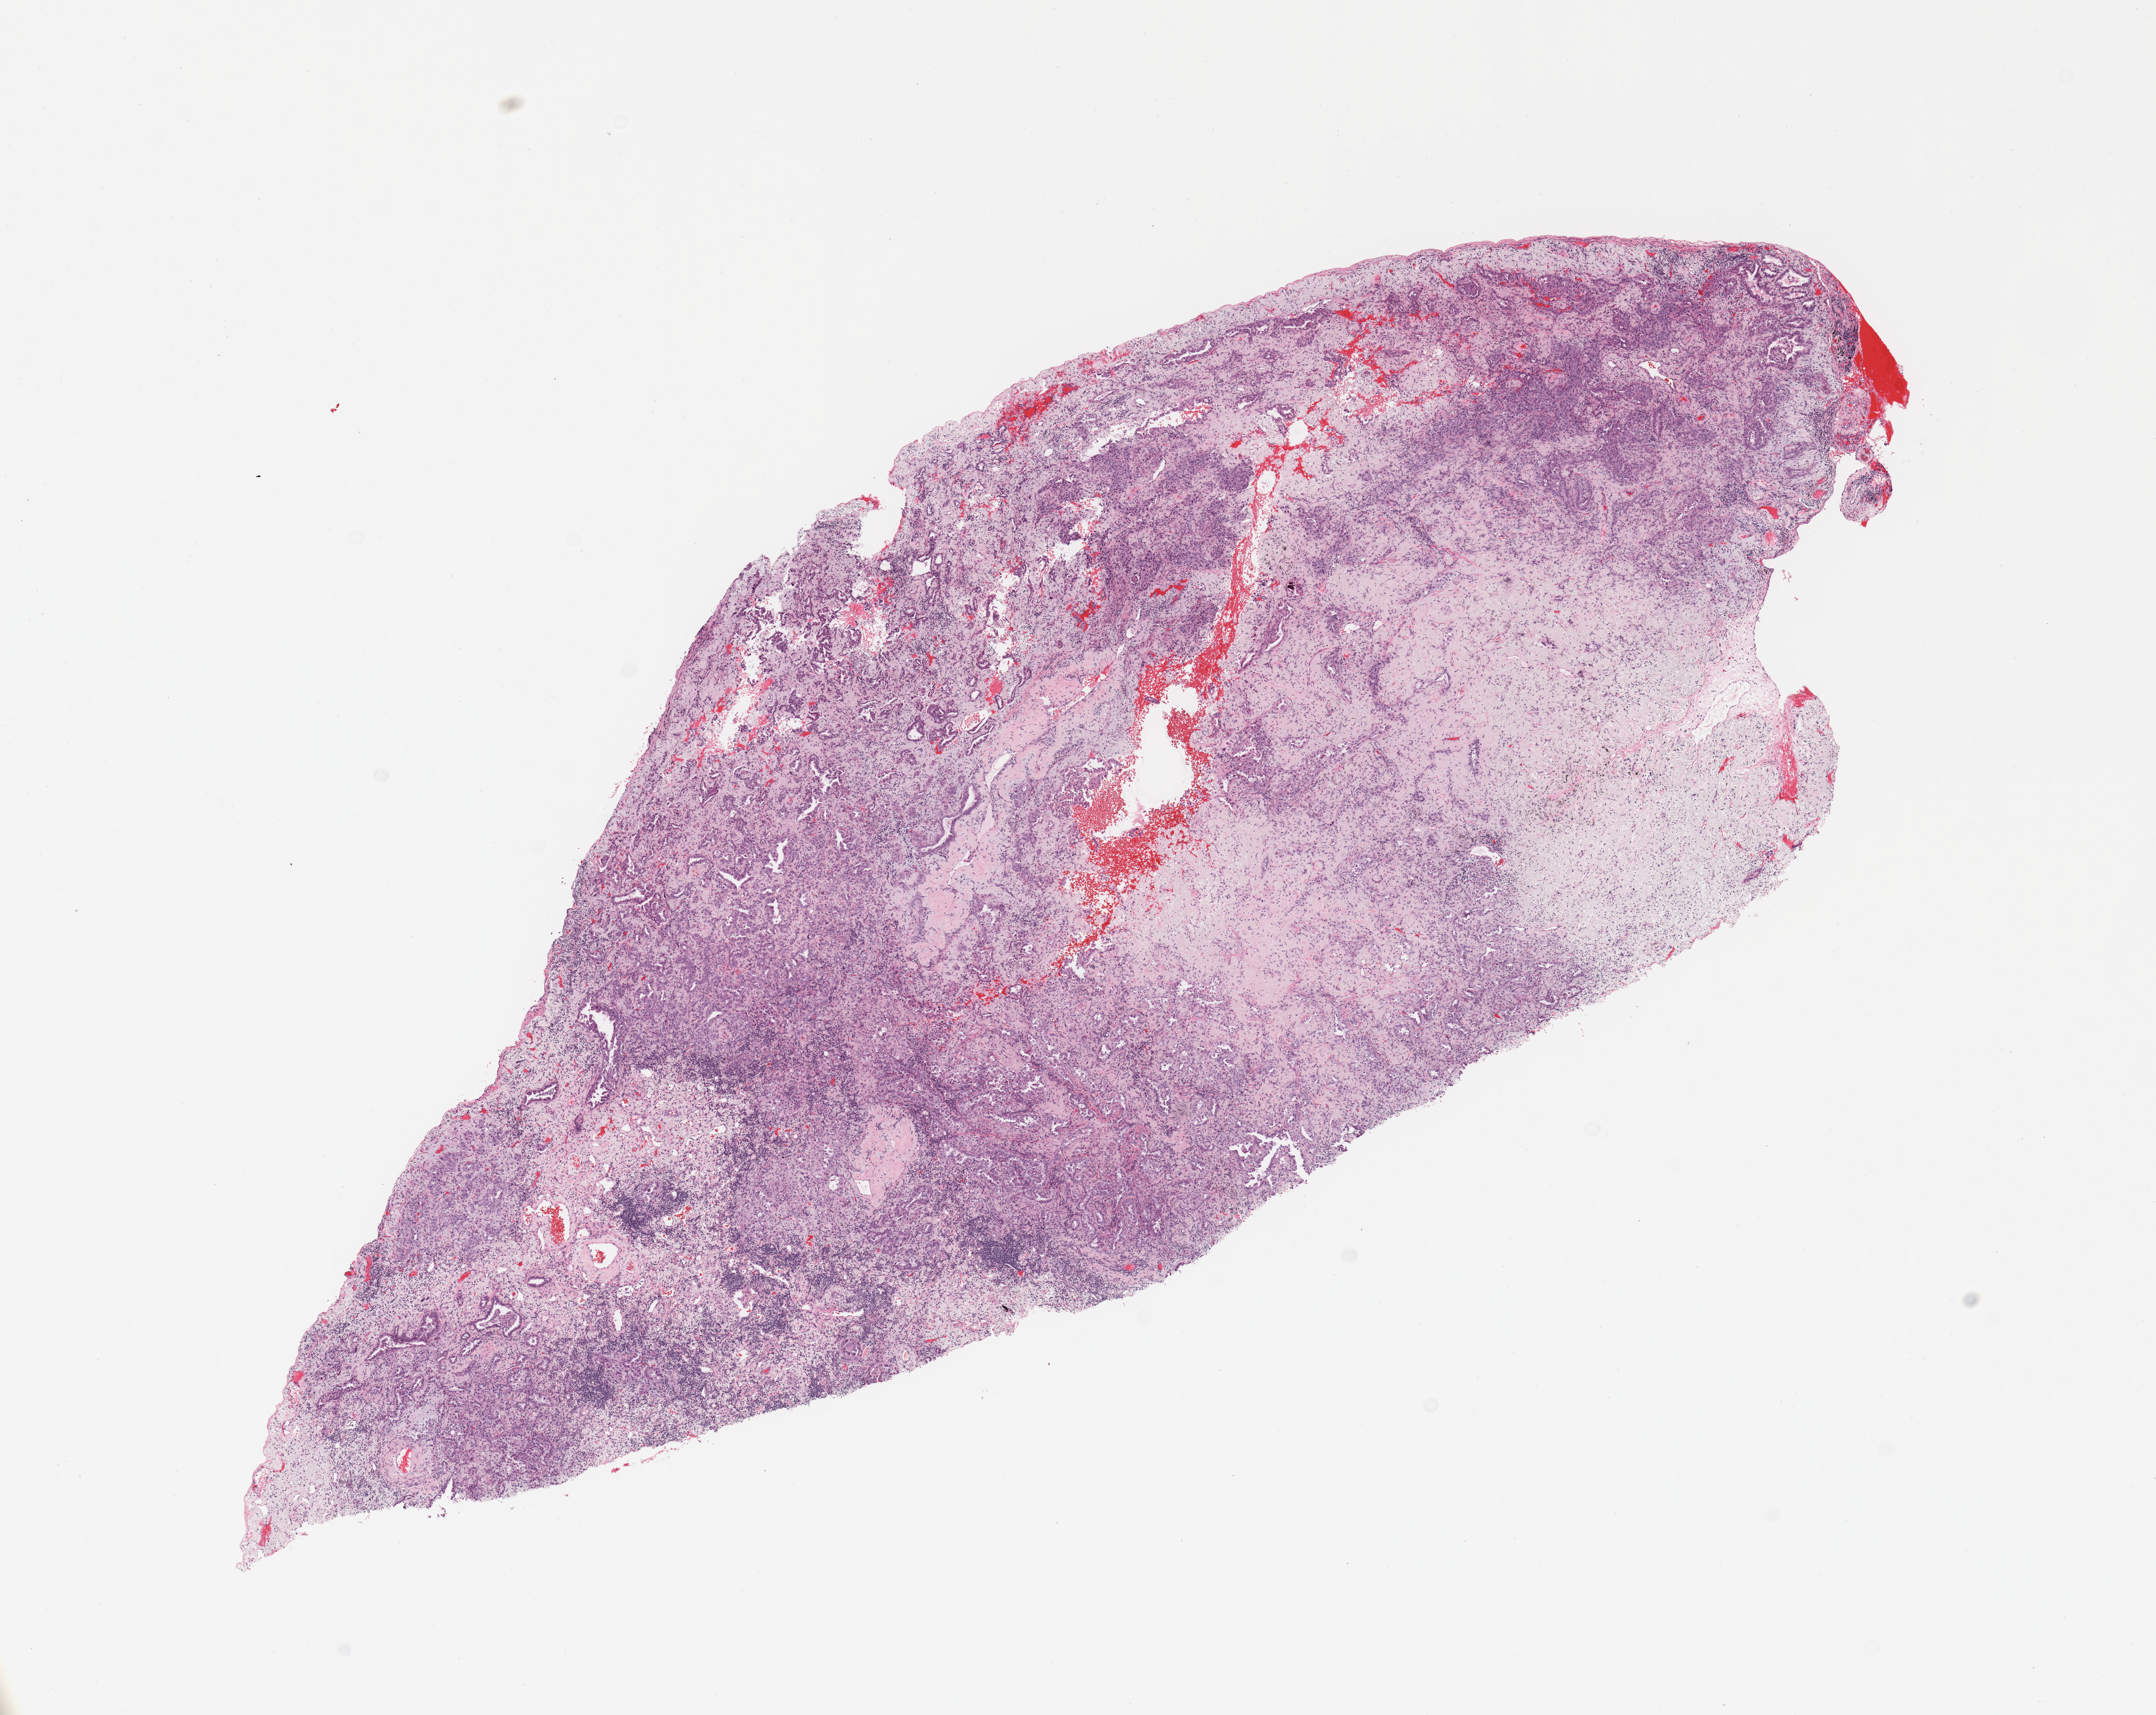
H&E whole-slide image — whole scanned area (about 12.8 x 10.2 mm) shown as a low-resolution overview, tumour tissue sample, sampled site: lung. Female, 66 y/o. Histologic grade: G2 (moderately differentiated). Composition of this section per pathologist review: tumour nuclei 65%, necrosis 2%.
Primary tumour site (as recorded): left lower lobe. Diagnosis: Adenocarcinoma, NOS. AJCC pathologic stage: IB.